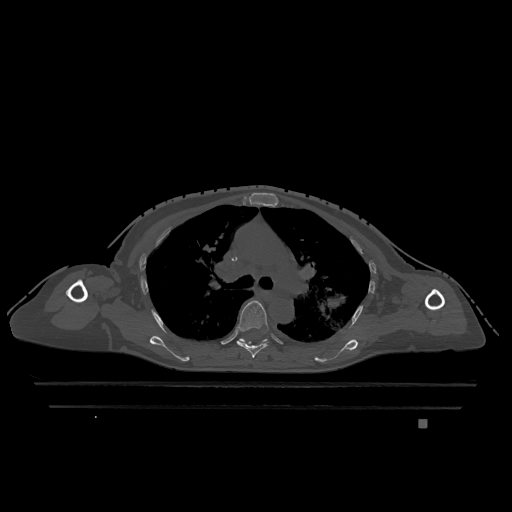
CT including the spine, one axial slice; slice 826 of 1317 in the series (ordered by position); bone window (W 1800 / L 400 HU); 0.5 mm slice thickness; 512 × 512 image matrix, field of view 500 × 500 mm. Female patient, age 74 years. Case-level facts recorded for this patient, not image findings: primary cancer: lung.
Structures marked on this image (semi-automatically segmented with operator editing):
- T5 vertebra: box from (x=237, y=300) to (x=269, y=358) px
- T6 vertebra: (x=238, y=338)–(x=268, y=344)